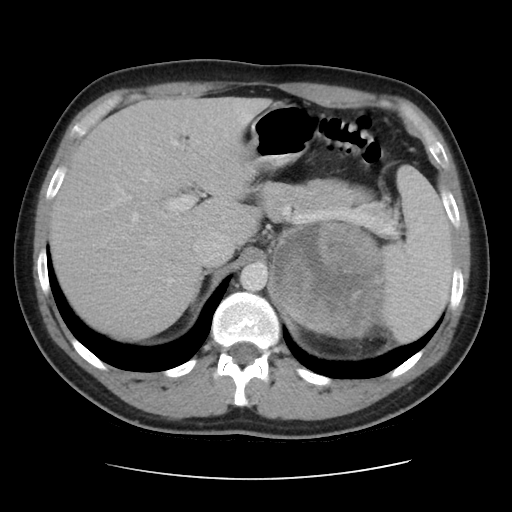
Contrast-enhanced abdominal CT, one axial slice. Position 32 of 48 along the scan axis. Reconstruction kernel STANDARD. Soft-tissue window (W 400 / L 40 HU). 5 mm slice thickness. 512 × 512 image matrix. Male patient, age 32 years. From the clinical record (not read from this slice): diagnosis: adrenocortical carcinoma; tumour side: left adrenal; tumour size at pathology: 14 cm; Ki-67 index: 67 %; stage (as recorded): 3.
Structures marked on this image (semi-automatic segmentation, software-assisted and operator-edited):
- mass: bounding box <274,223,379,335> (left, top, right, bottom; pixels)